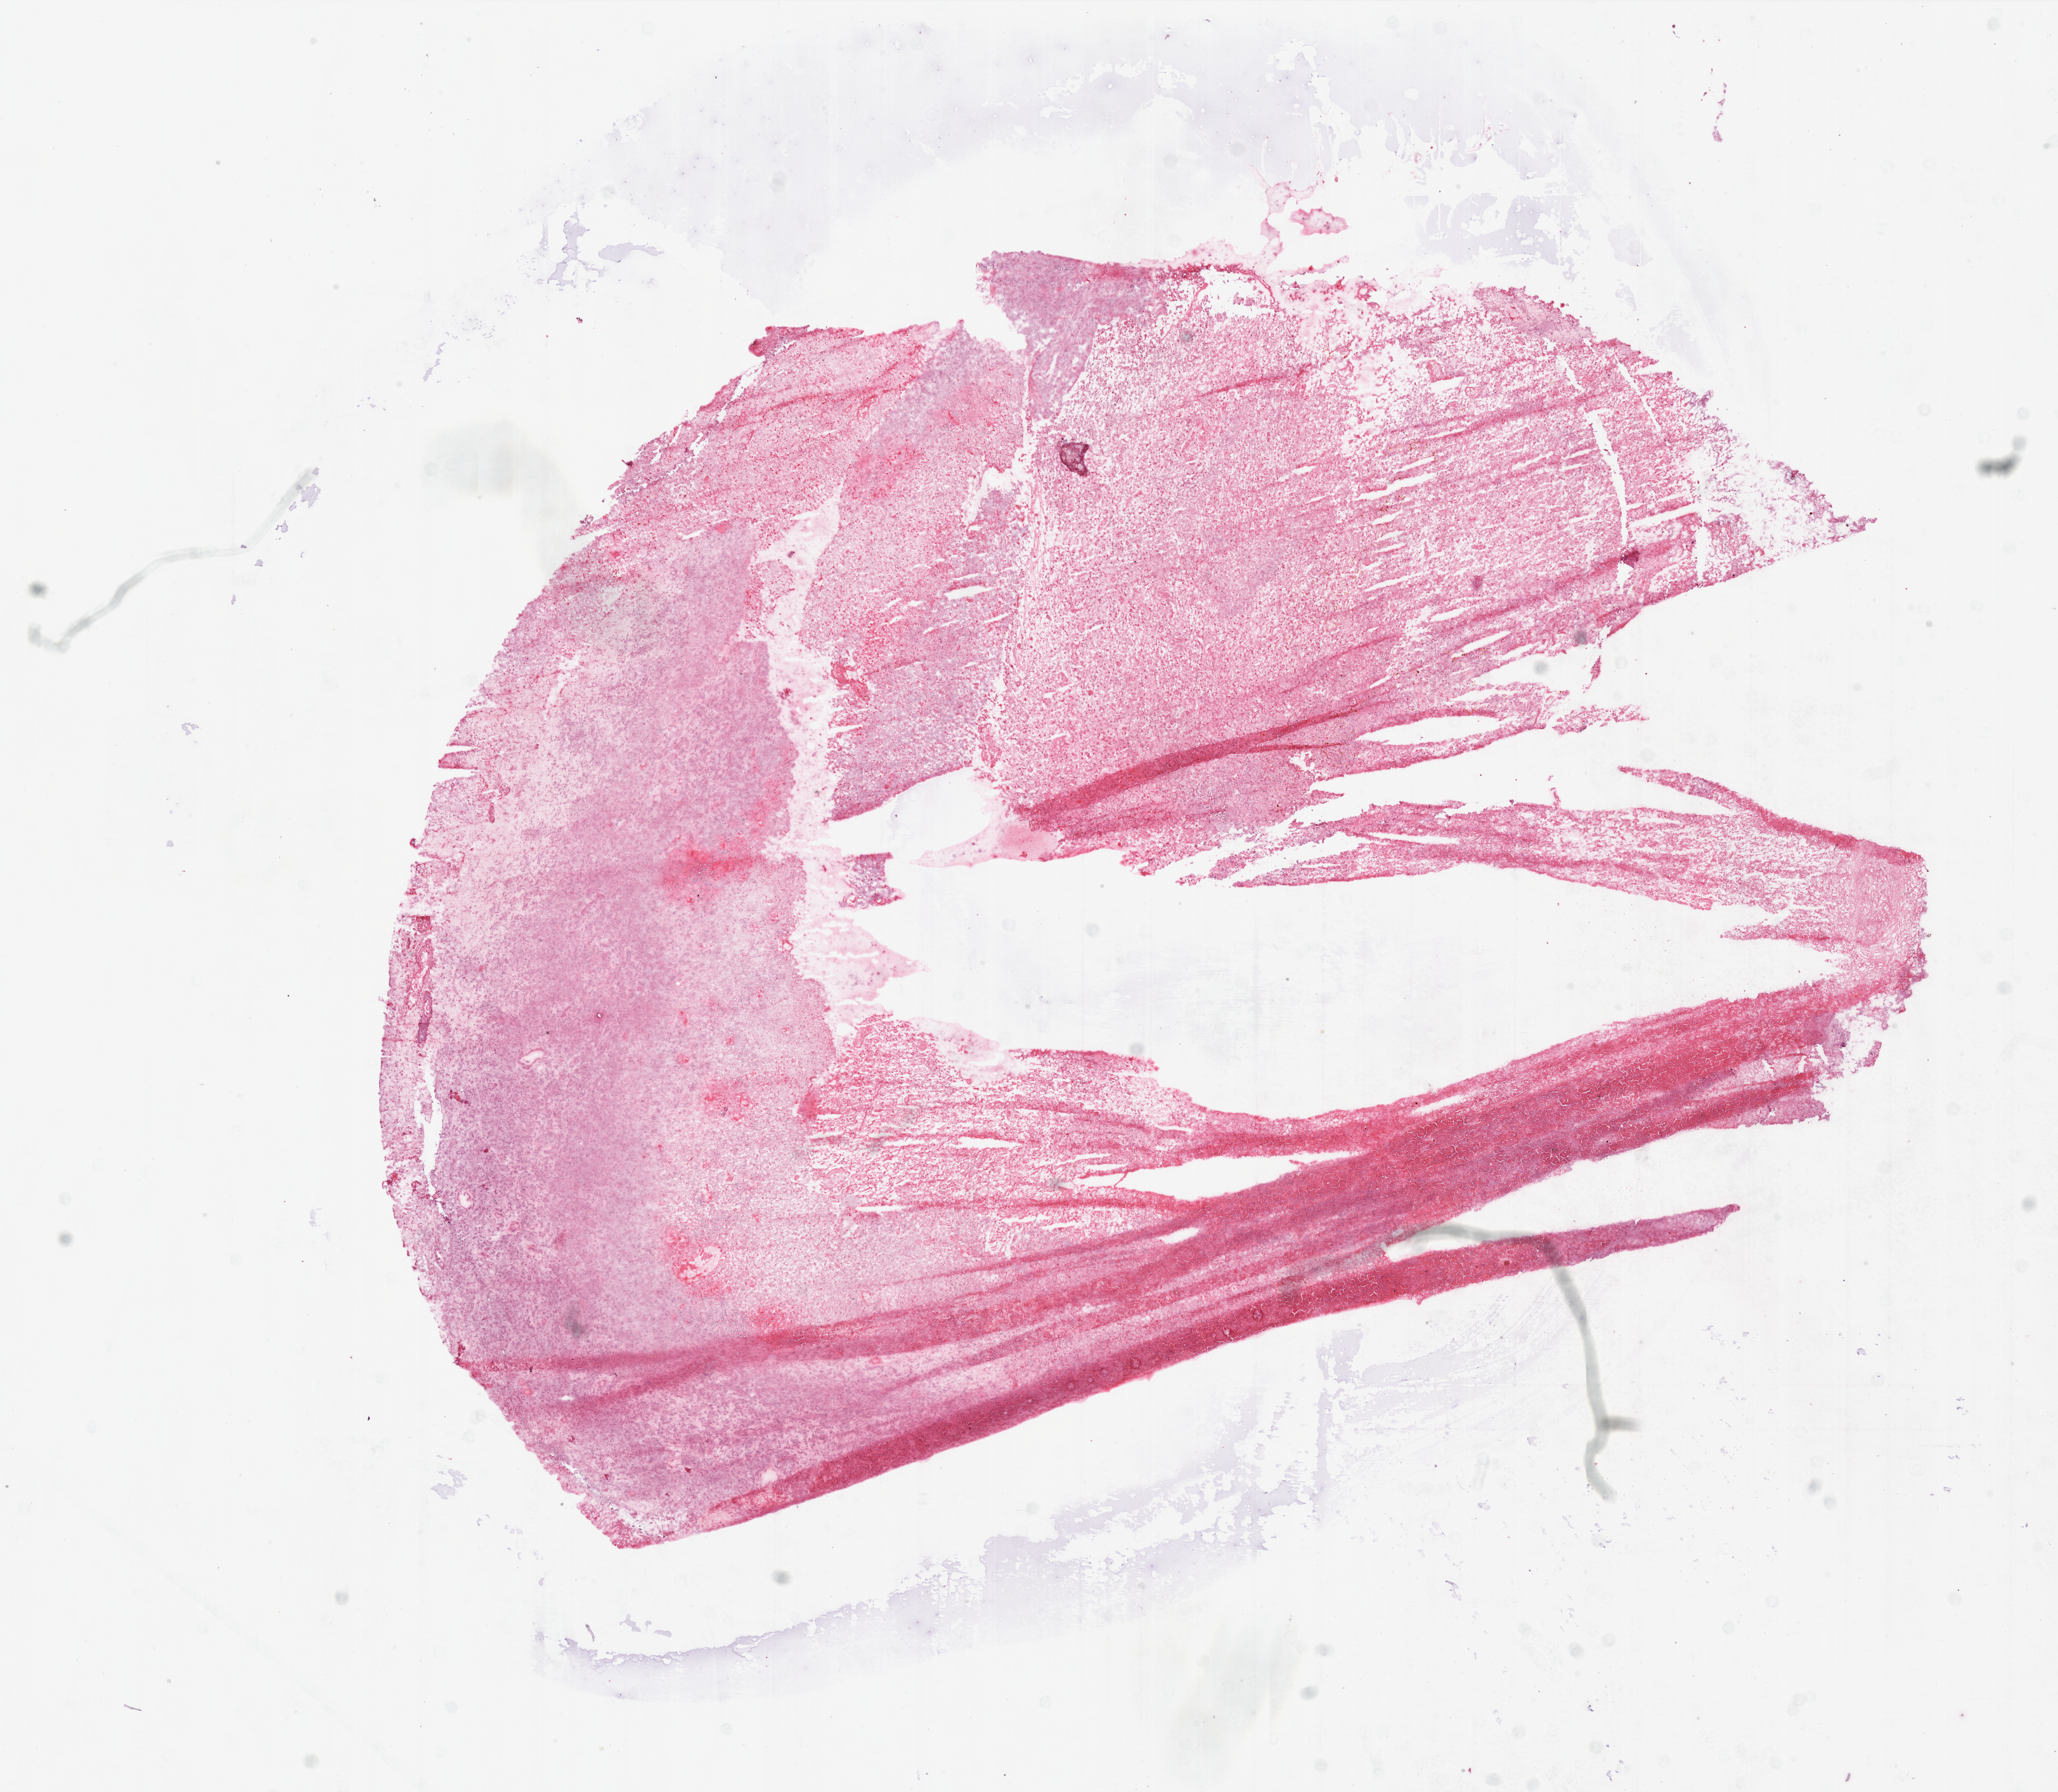
Whole-slide histology image, Hematoxylin and eosin (H&E) stained — low-resolution overview of the scanned area, about 13.0 x 11.3 mm (slide scanned at 20x). Frozen section. Primary tumour sample from the brain. Male patient; age at initial diagnosis 40 years. Slide review estimates, as recorded: tumour cells 25%, tumour nuclei 99%, normal cells 0%, stromal cells 0%, necrosis 75%.
- histologic diagnosis: Glioblastoma